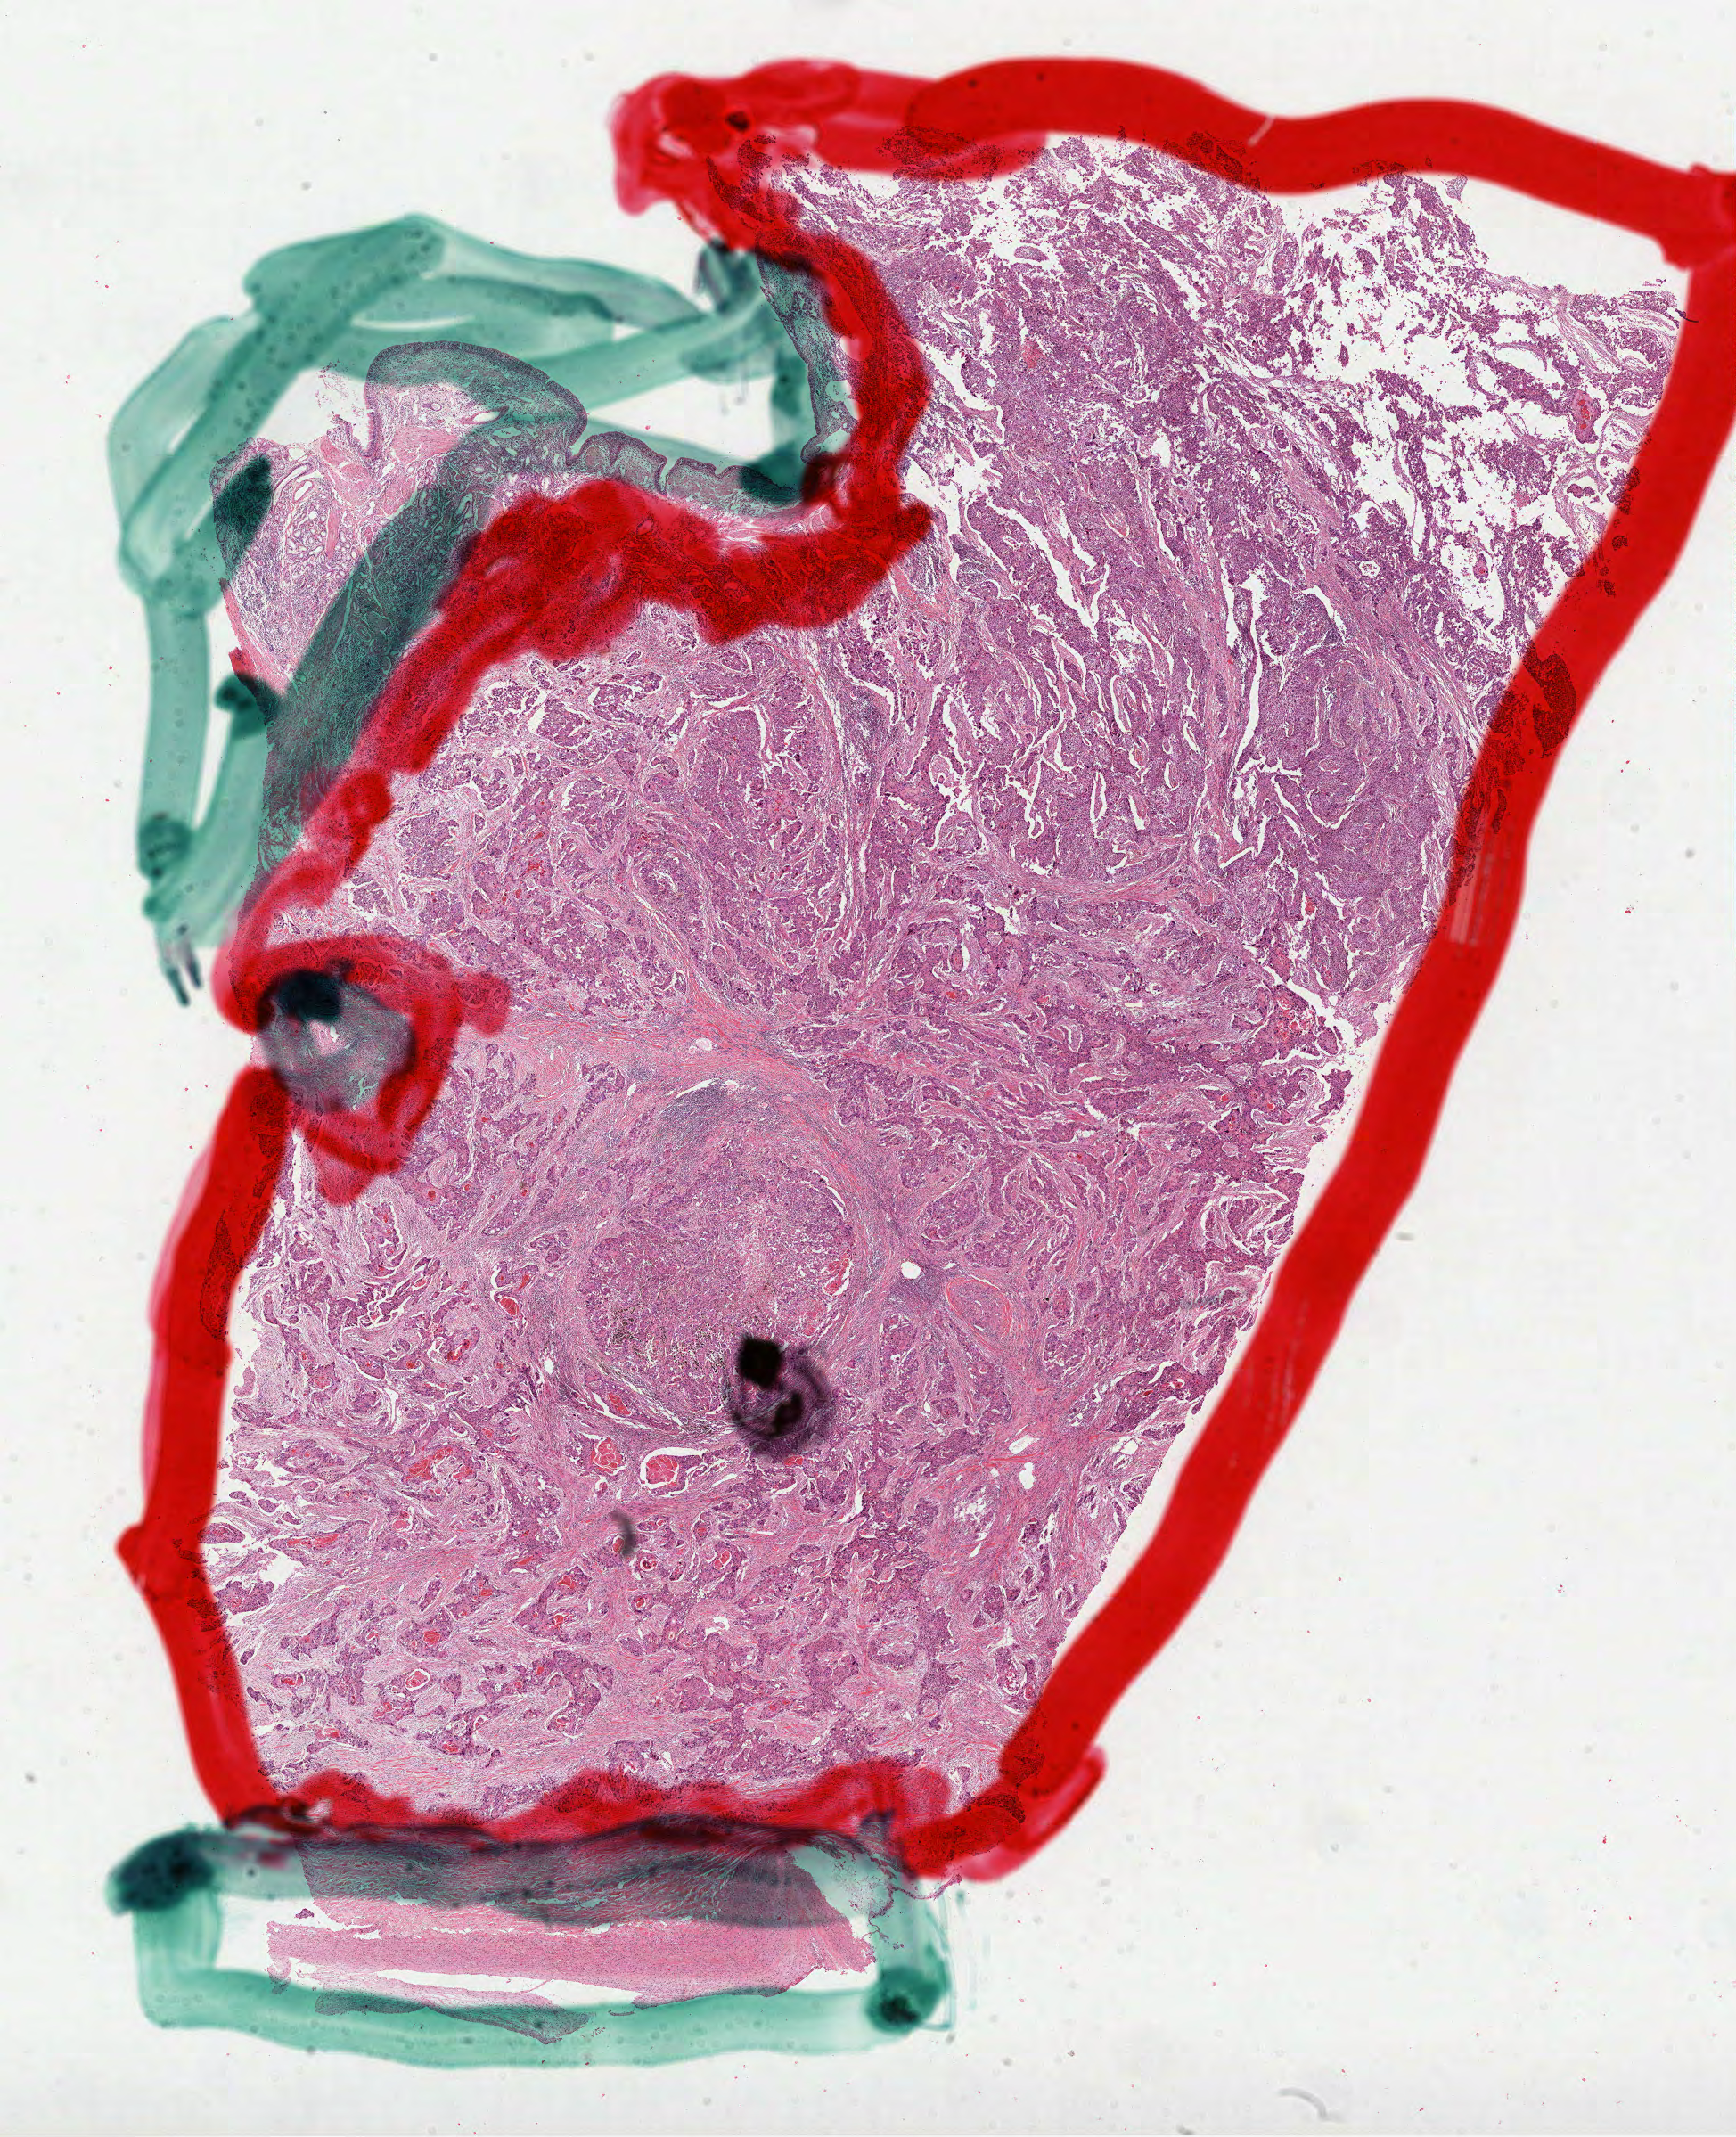
H&E-stained whole-slide image, low-resolution overview of the scanned area, about 15.7 x 19.3 mm. FFPE section. Sample: primary tumour, lung. Male patient; age at initial diagnosis 57 years.
AJCC pathologic stage: IB (7th edition). Pathologic diagnosis: Squamous cell carcinoma, NOS (lower lobe, lung).